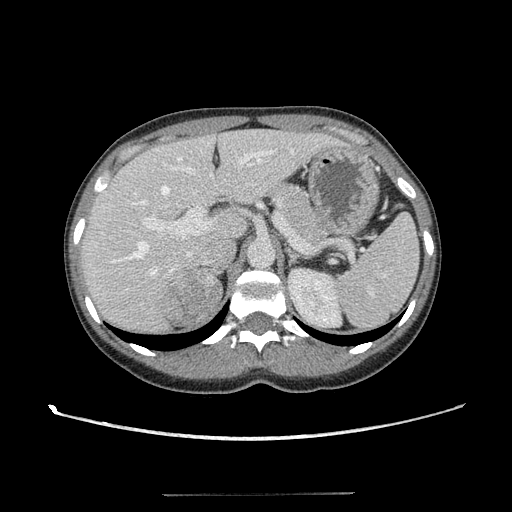
Contrast-enhanced abdominal CT, one axial slice; reconstruction kernel STANDARD; intravenous contrast given; soft-tissue window (W 400 / L 40 HU); 2.5 mm slice thickness; 512 × 512 image matrix, field of view 365 × 365 mm. Patient: female, 35 years. Case-level facts recorded for this patient, not image findings: diagnosis: adrenocortical carcinoma; tumour side: right adrenal; tumour size at pathology: 3 cm; Ki-67 index: 21 %; stage (as recorded): 3.
Structures marked on this image (semi-automatic segmentation, software-assisted and operator-edited):
- mass: bounding box [x1, y1, x2, y2] px = [161, 273, 222, 326]